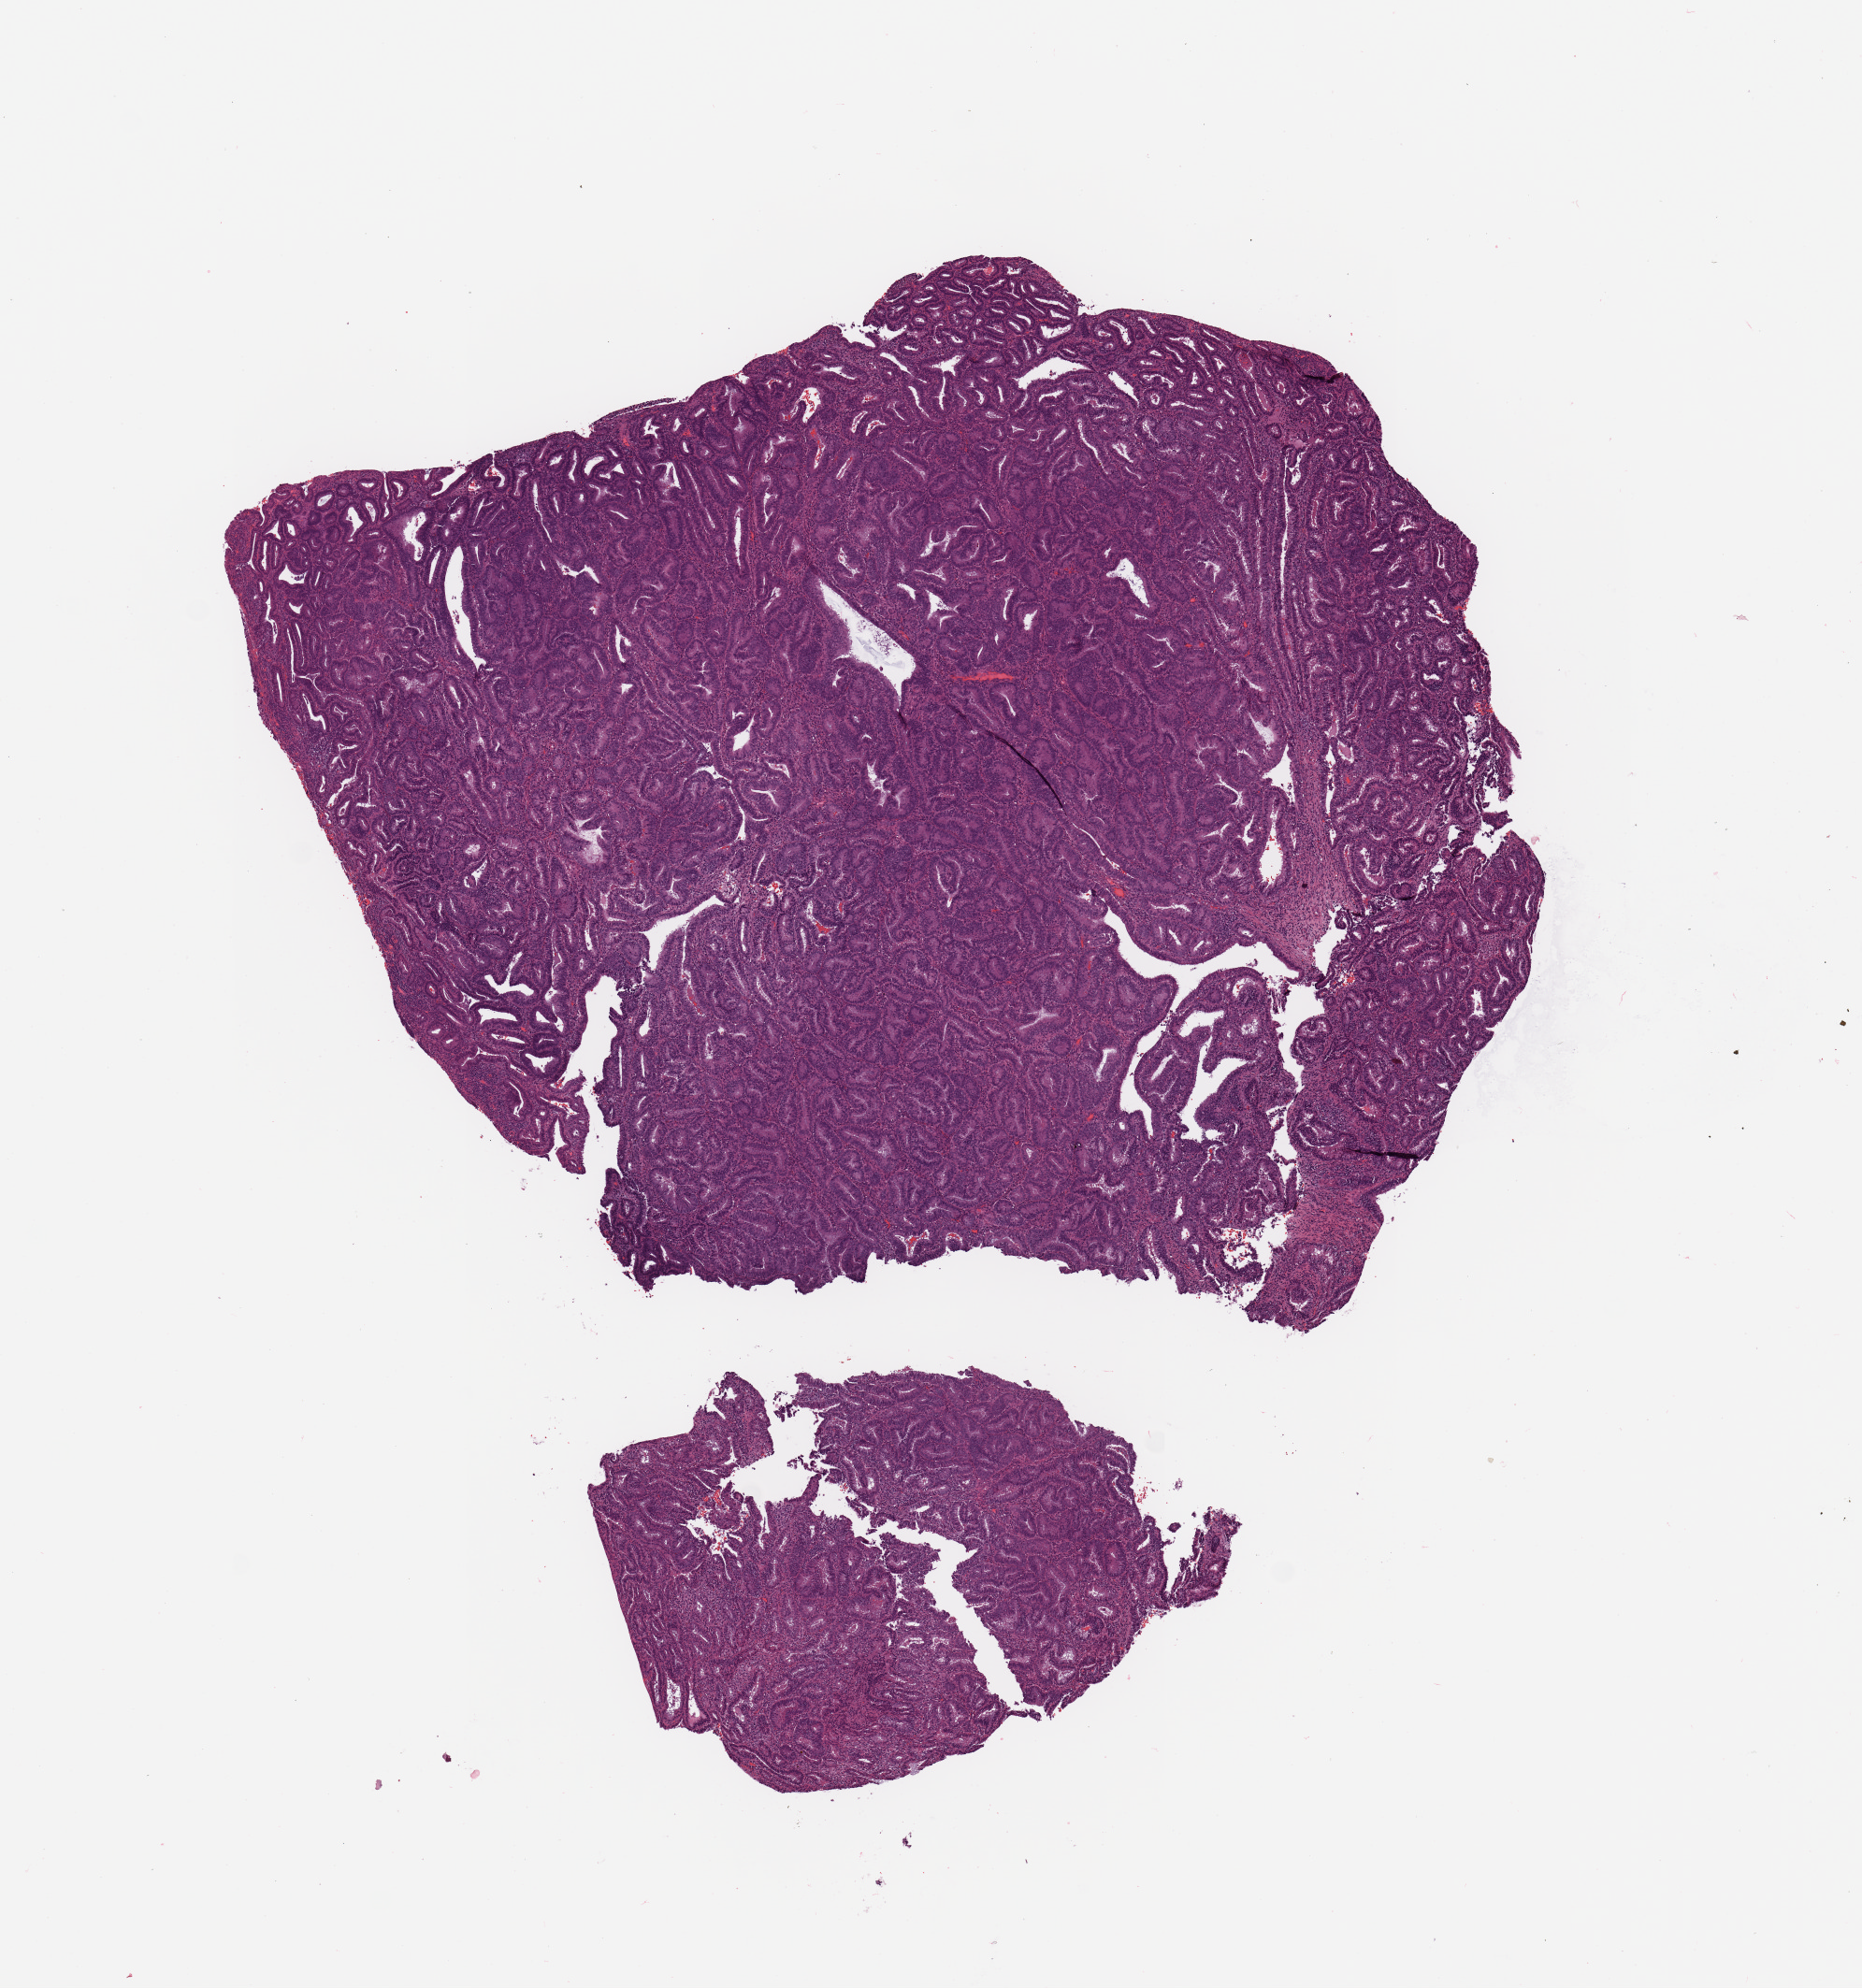
Digitized H&E-stained tissue section (whole slide) — low-resolution overview of the scanned area, about 7.9 x 8.4 mm. Tumour tissue sample, uterus. Patient: female, age 55 years. Histologic grade: G1 (well differentiated).
- AJCC pathologic stage: I
- histologic diagnosis: Endometrioid adenocarcinoma, NOS